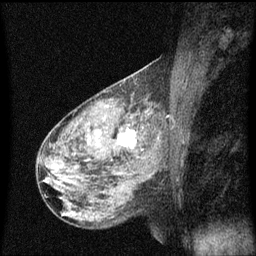
Breast MRI (dynamic contrast-enhanced), one sagittal slice; position 36 of 60 along the scan axis; dynamic contrast-enhanced series, image 2 of 3 at this slice position (ordered by acquisition); 1.5 T; TE 4.2 ms, TR 8 ms; 256 × 256 image matrix. Female patient, age 50 years.
Structures marked on this image (semi-automatically segmented with operator editing):
- analysis volume of interest (the breast-tissue region the enhancement analysis was run in; not a lesion): bounding box <106,118,148,159> (left, top, right, bottom; pixels)
- tumour enhancement mask (voxels above the 70 % enhancement threshold inside the analysis volume of interest): <117,130,136,149>